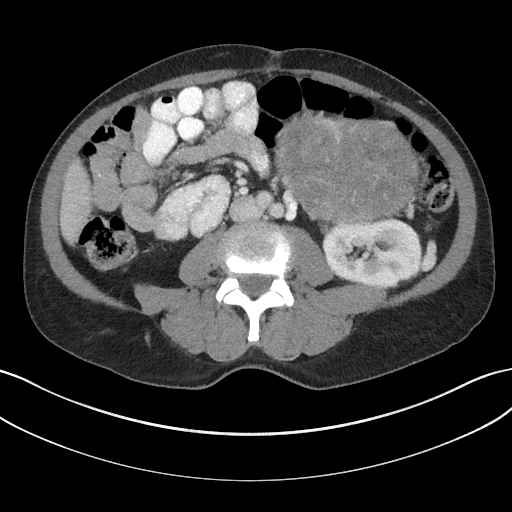
Contrast-enhanced abdominal CT, one axial slice. Position 78 of 147 along the scan axis. 100 kVp. Intravenous contrast given. Soft-tissue window (W 400 / L 40 HU). 512 × 512 image matrix, field of view 384 × 384 mm. Male patient, age 58 years. From the clinical record (not read from this slice): diagnosis: adrenocortical carcinoma; tumour side: left adrenal; tumour size at pathology: 22 cm; Ki-67 index: 26 %; stage (as recorded): 2.
Annotated regions visible in this slice (semi-automatically segmented with operator editing):
- mass: bounding box (x1, y1, x2, y2) in pixels: (278, 111, 416, 220)